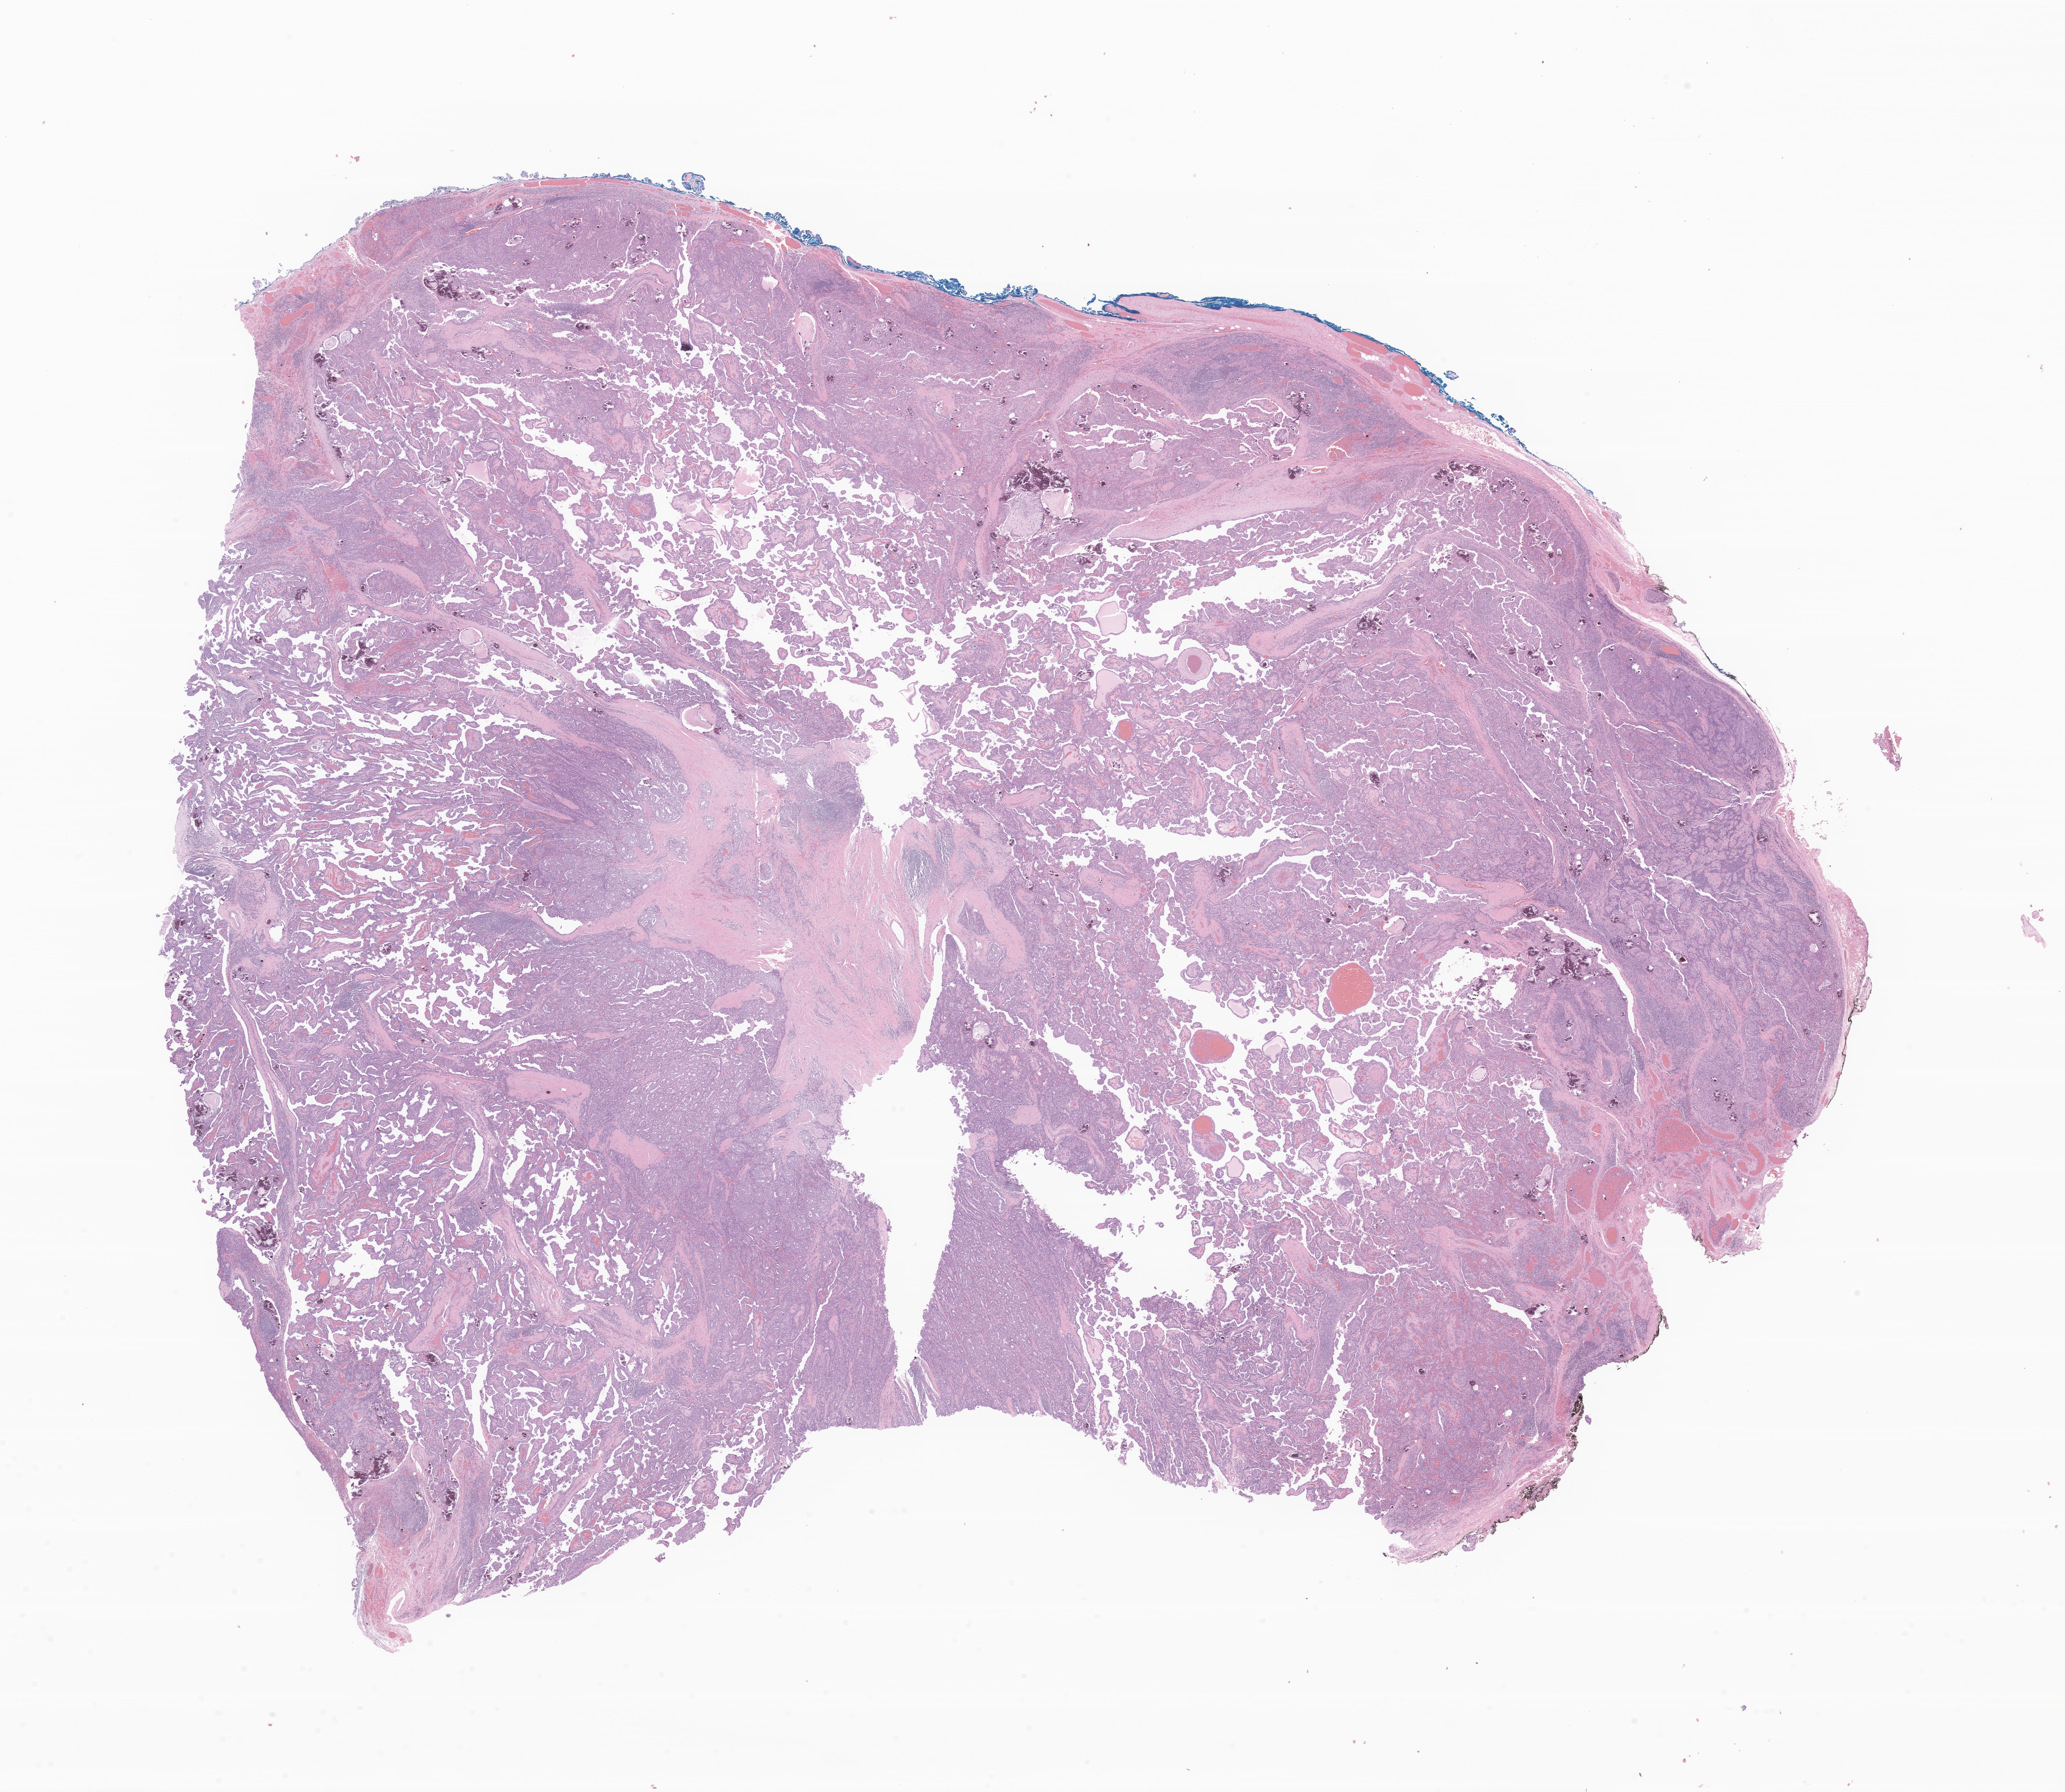
Digitized H&E-stained section of tumor tissue from the thyroid — a low-resolution overview of the entire scanned area, about 24.7 x 21.5 mm, FFPE section. Female patient, age 184 months (15 years 4 months).
• diagnosis (ICD-O-3 morphology term): Papillary carcinoma, NOS